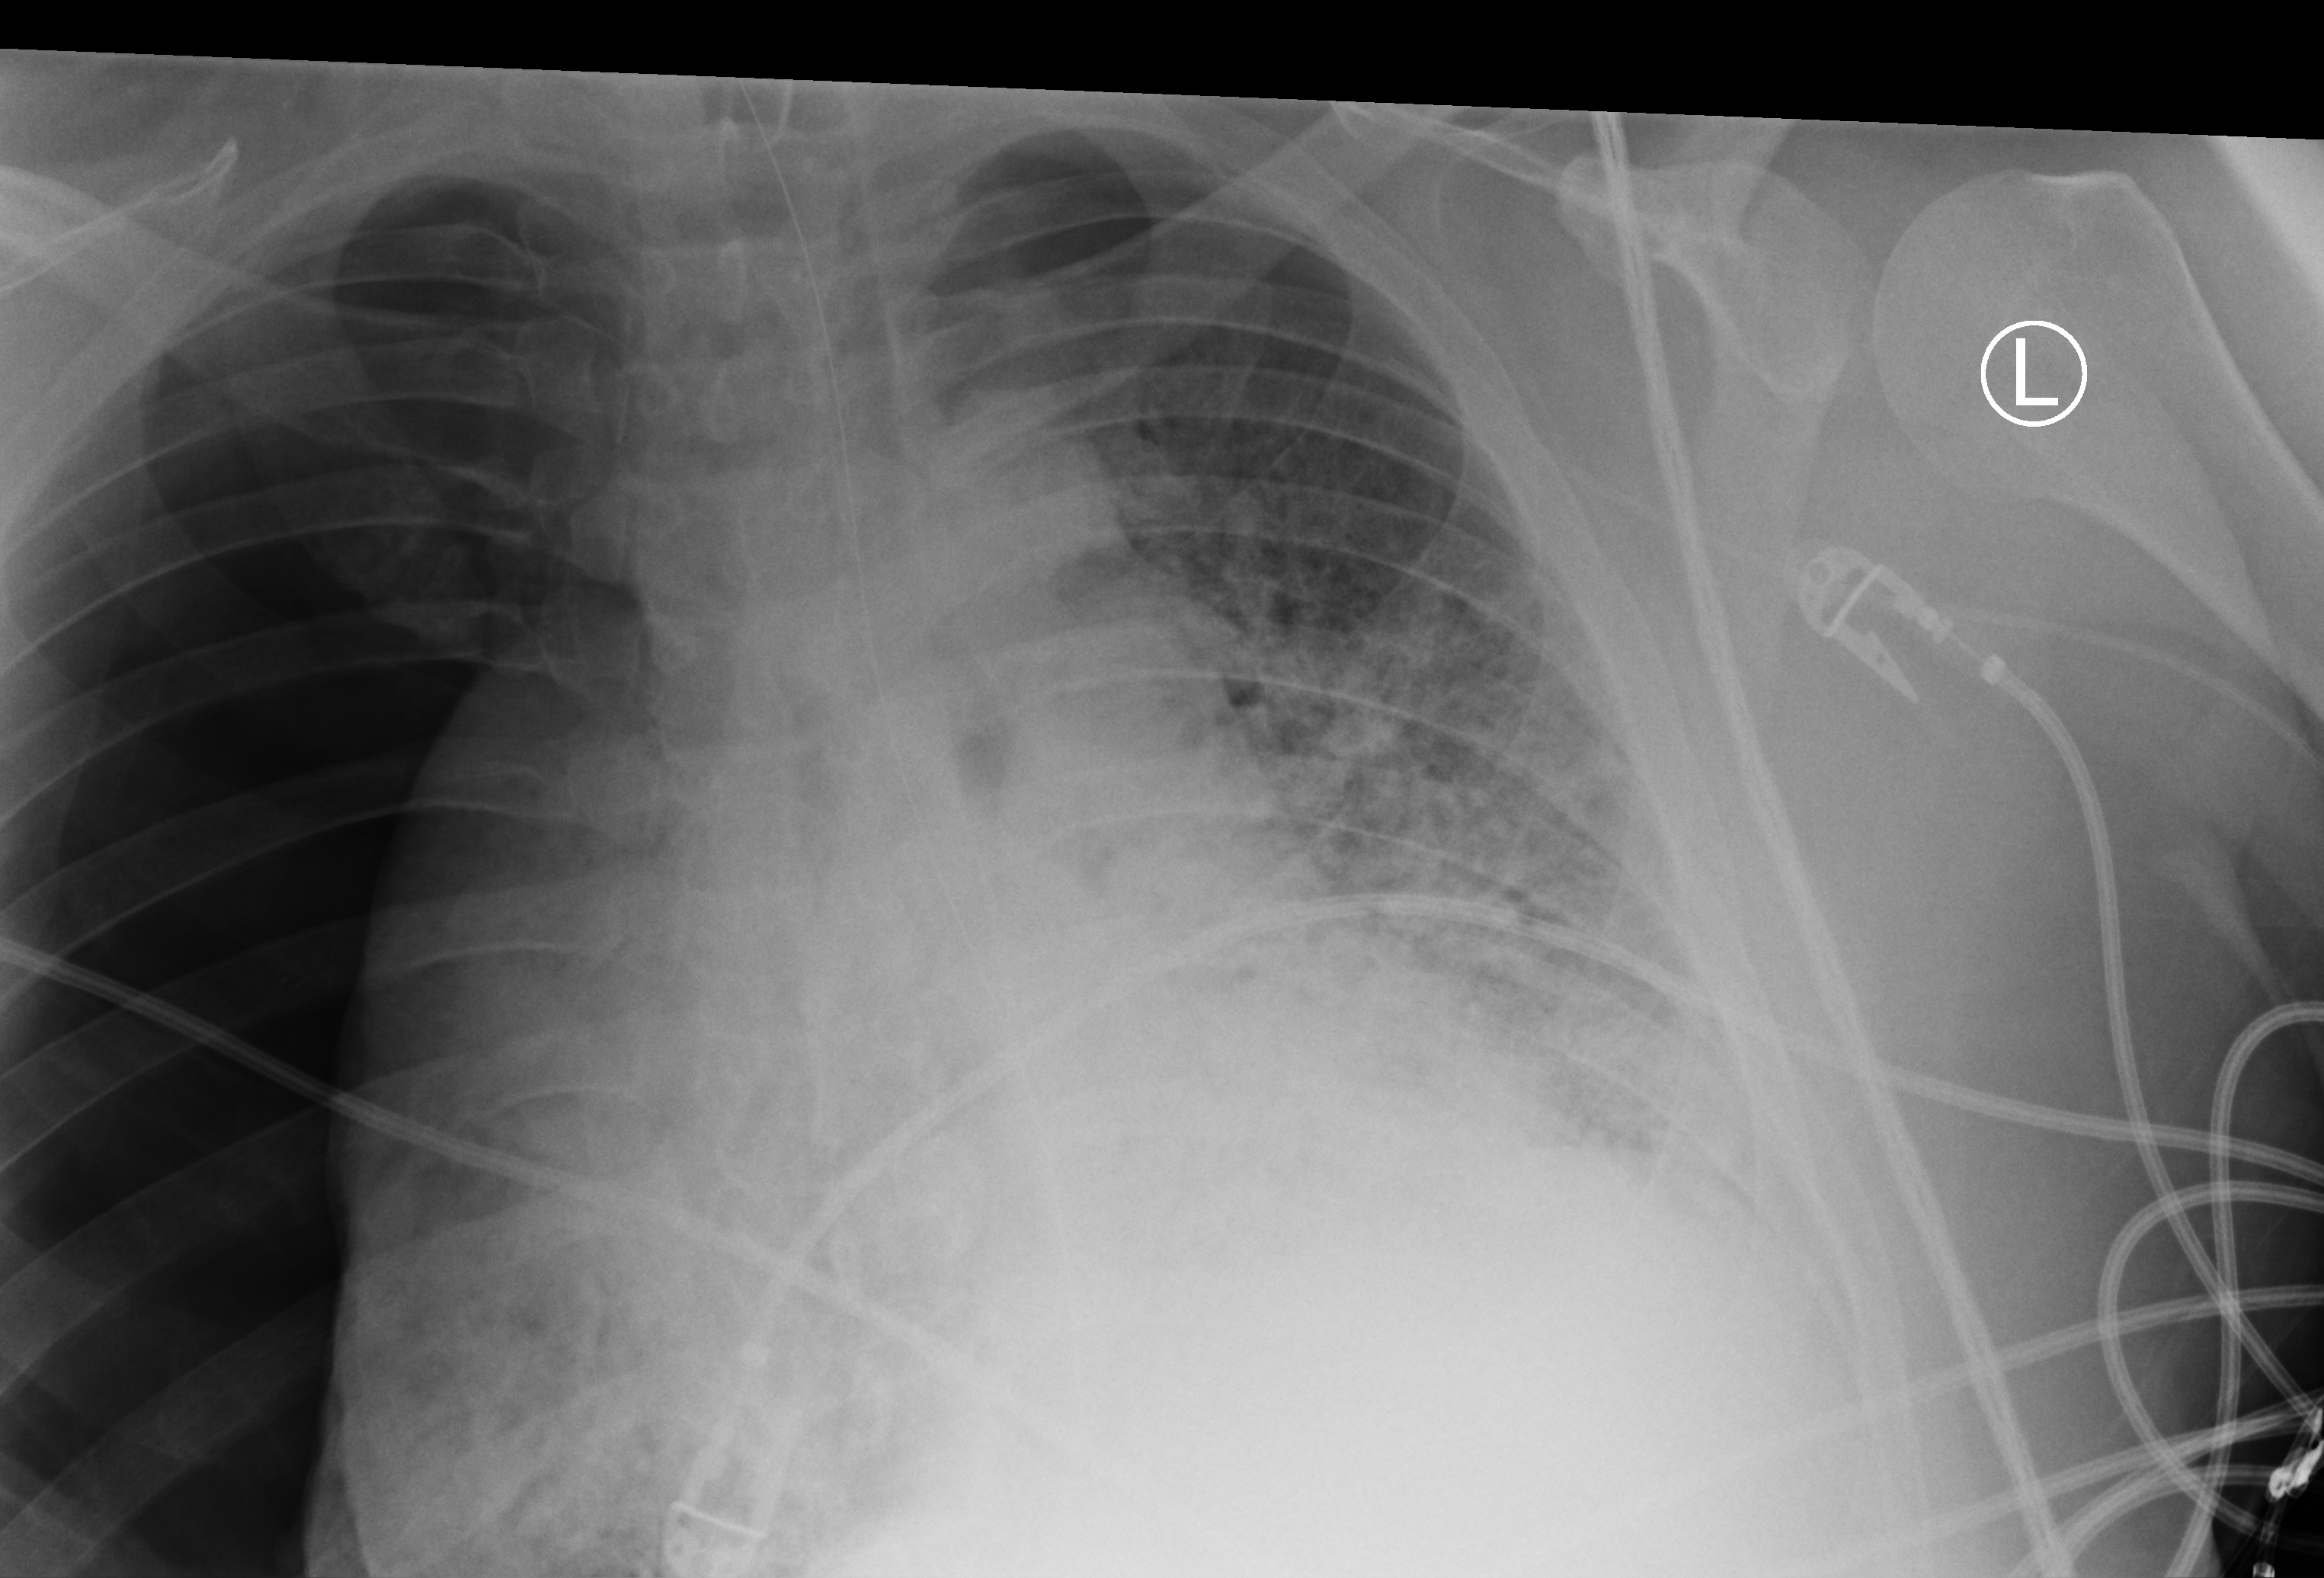
Portable chest radiograph, anteroposterior (AP) projection. Patient hospitalised with COVID-19, aged 18–59 years.
Admission-level facts for this patient (not findings on this image; timing relative to this image not recorded): admitted to intensive care during this hospital stay: yes.